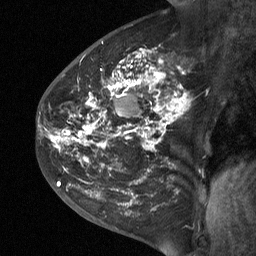
Breast MRI (dynamic contrast-enhanced), one sagittal slice. Slice 35 of 64 in the series (ordered by position). Dynamic contrast-enhanced study with each time point stored as its own series, time point 2 of 3 at this slice position (early post-contrast, ordered by acquisition time). 1.5 T. TE 4.8 ms, TR 27 ms. 256 × 256 image matrix, field of view 200 × 200 mm. Female patient, age 42 years. From the clinical record (not read from this slice): setting: breast cancer imaged before/during neoadjuvant chemotherapy; receptor status: triple-negative.
Structures marked on this image (semi-automatic segmentation, software-assisted and operator-edited):
- analysis volume of interest (the breast-tissue region the enhancement analysis was run in; not a lesion): box from (x=43, y=29) to (x=201, y=190) px
- tumour enhancement mask (voxels above the 90 % enhancement threshold inside the analysis volume of interest): (x=53, y=50)–(x=187, y=185)